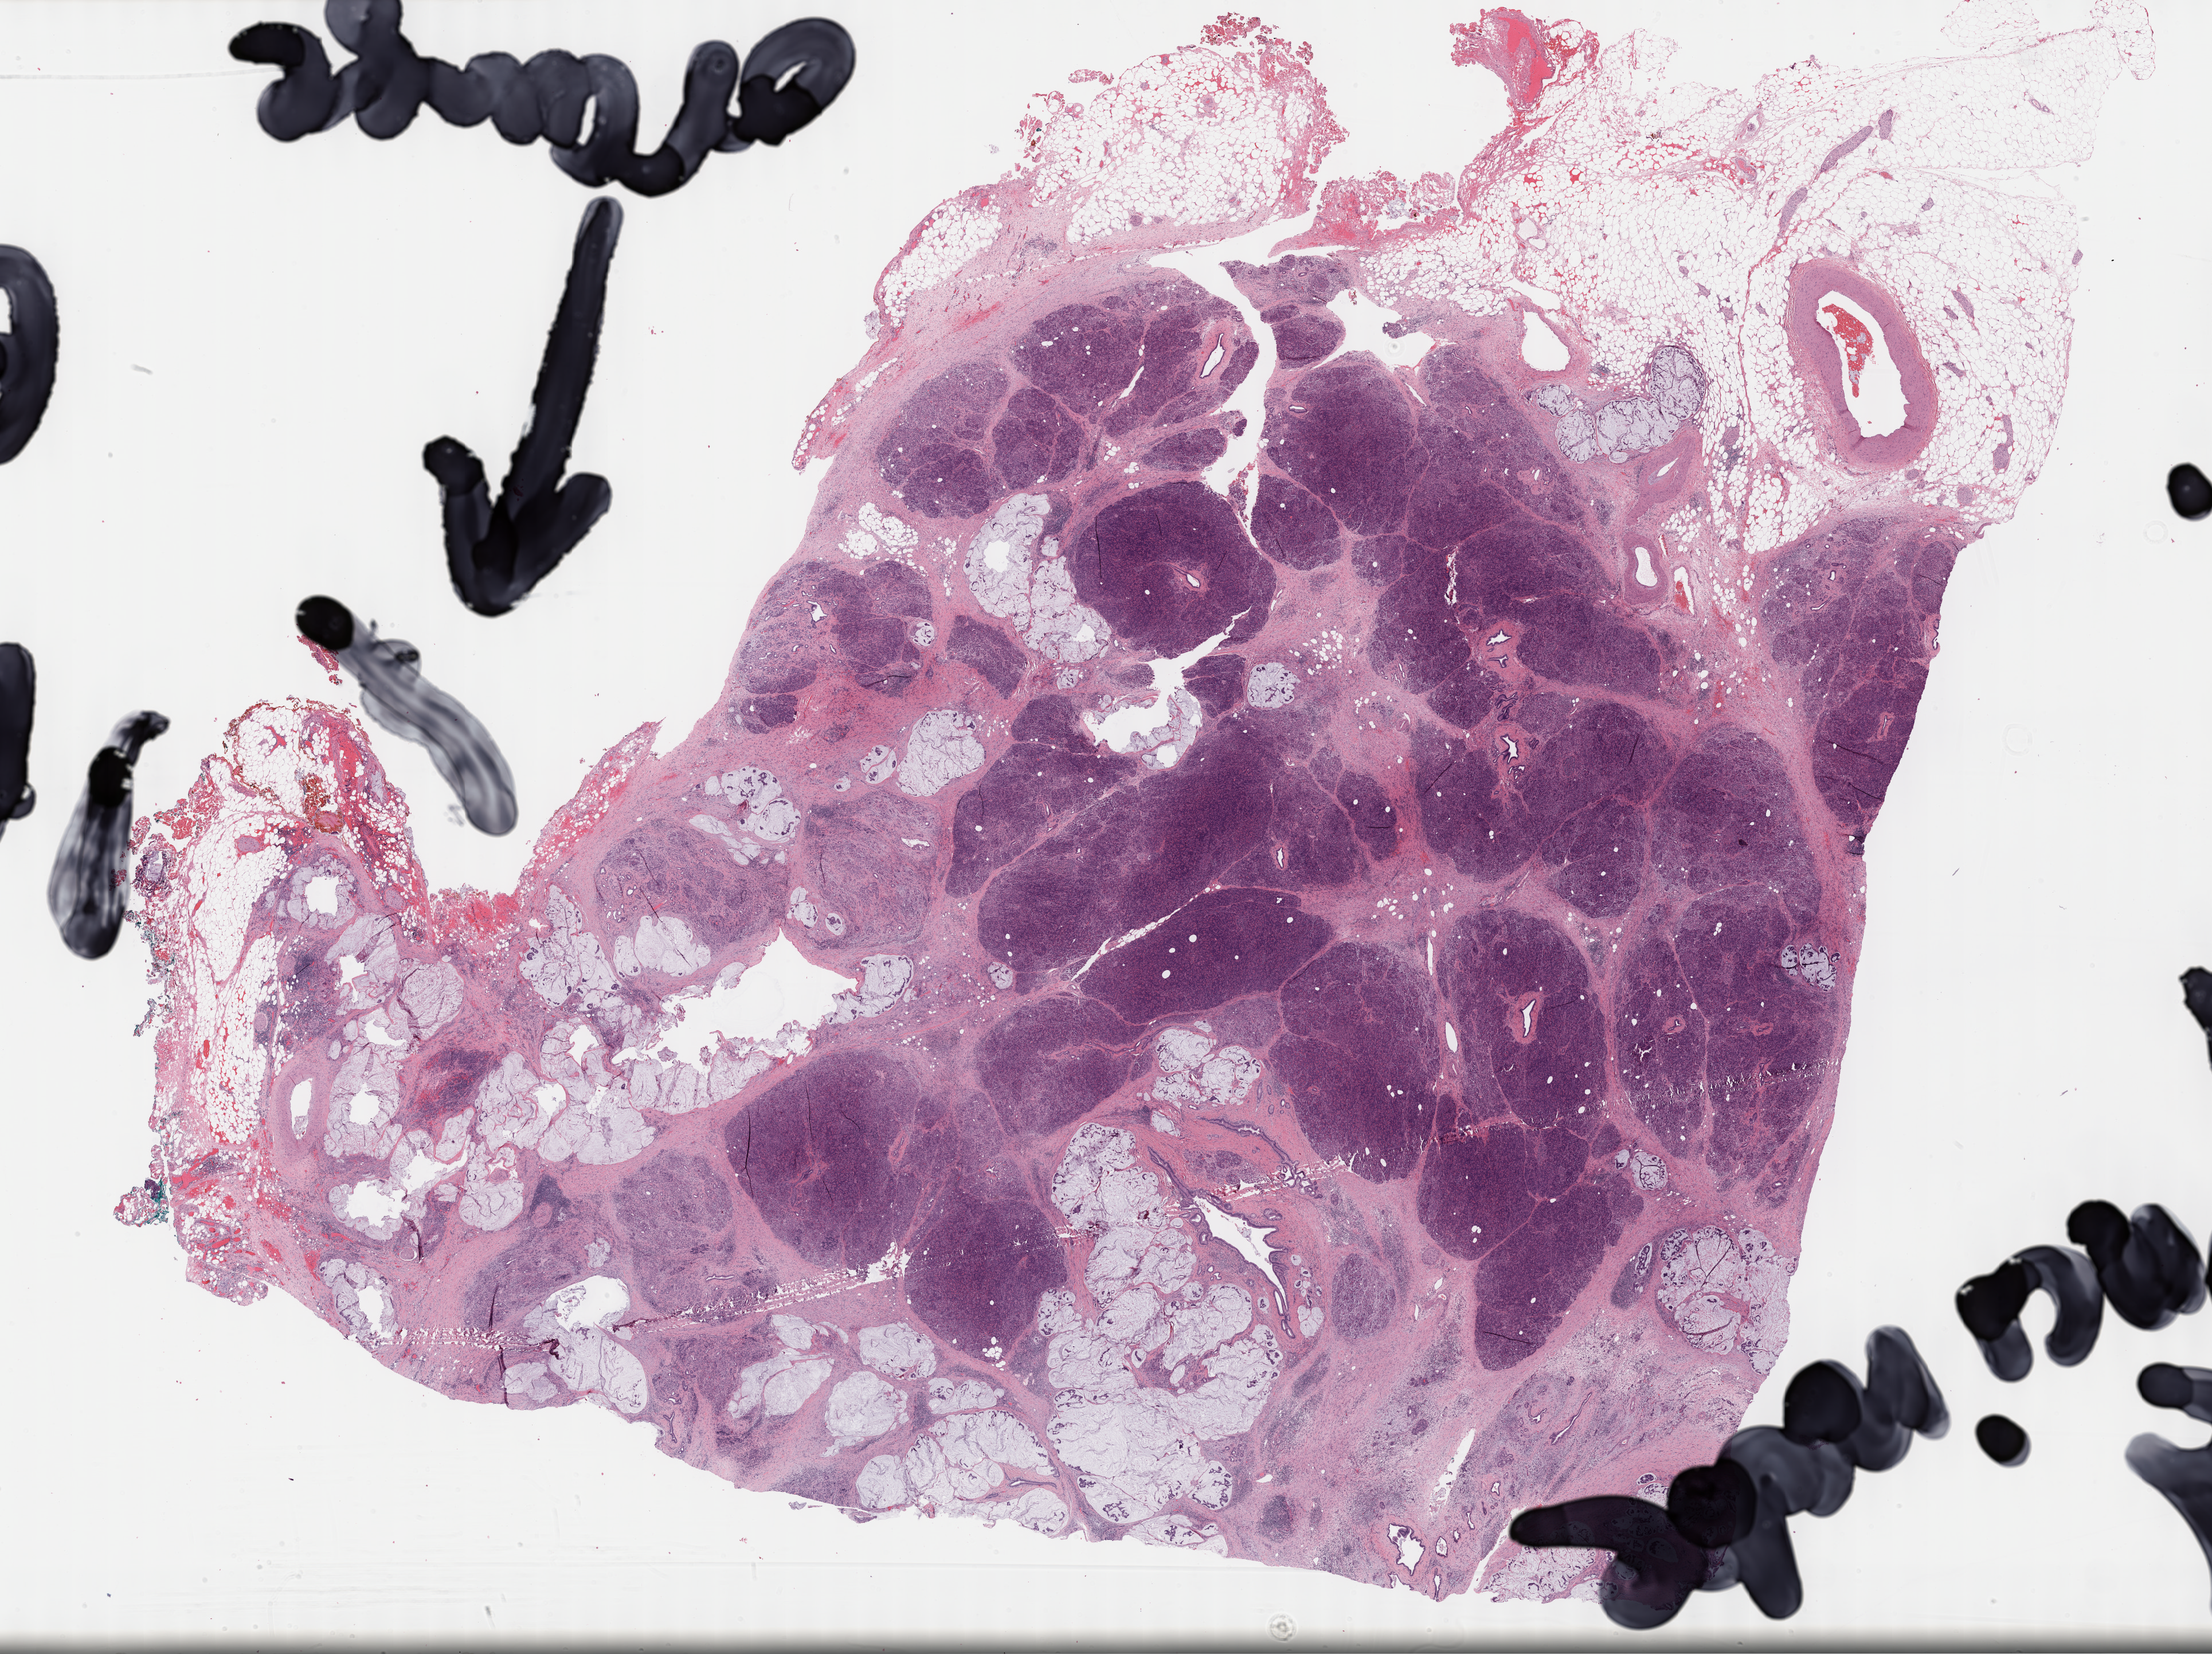
Whole-slide histology image, Hematoxylin and eosin (H&E) stained — a low-resolution overview of the entire scanned area, about 31.2 x 23.3 mm, FFPE section, primary tumour sample from the pancreas. Male, age 65 years at initial diagnosis. Histologic grade: G1 (well differentiated).
* lymph nodes positive (case pathology): 7 of 11 examined
* AJCC pathologic stage: IIB (7th edition)
* diagnosis: Mucinous adenocarcinoma (head of pancreas)